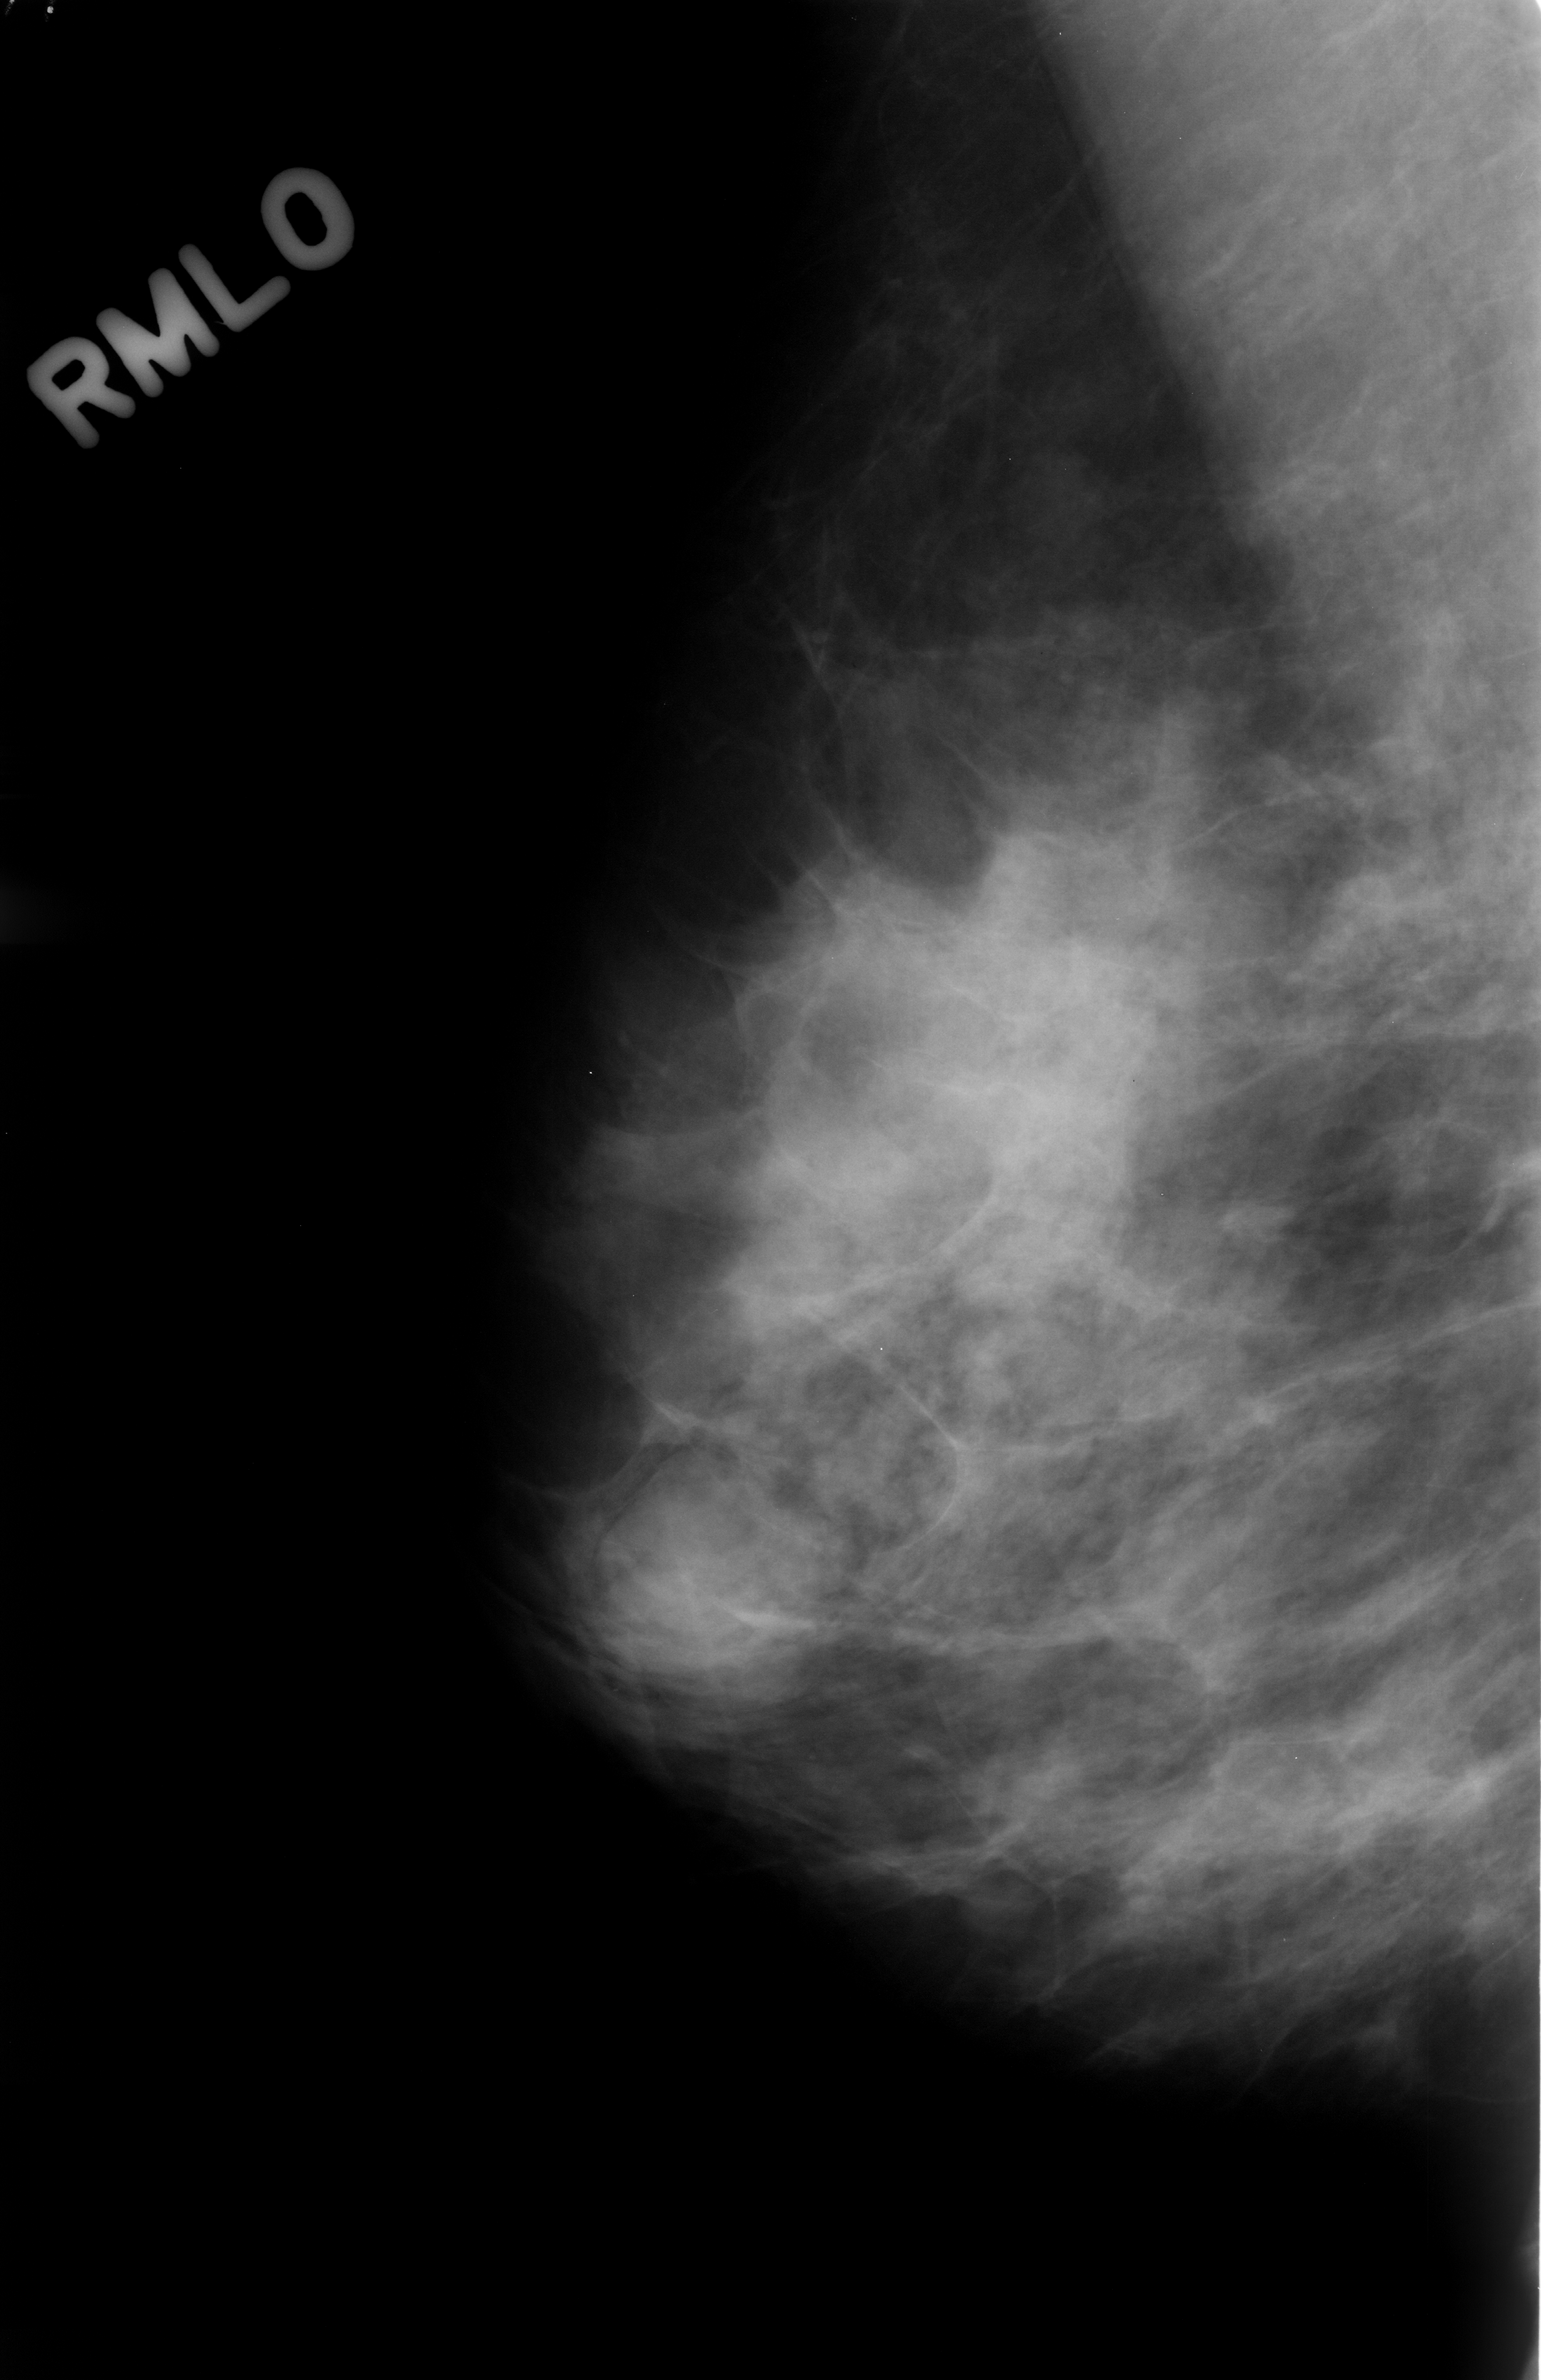
Scanned film-screen mammogram; right breast; mediolateral oblique (MLO) view; BI-RADS breast density category 2 (scale 1–4); 1541 × 2380 image matrix.
Expert-marked regions of interest on this film, with their recorded descriptors:
- mass, shape lobulated, margins circumscribed; BI-RADS assessment category 4; subtlety rating 4 on a 1 (subtle) to 5 (obvious) scale; pathology (as recorded): benign: bounding box (x1, y1, x2, y2) in pixels: (593, 1465, 818, 1696)